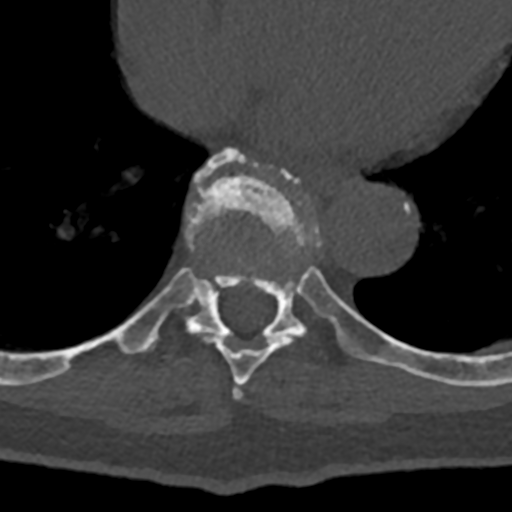
CT including the spine, one axial slice; position 681 of 797 along the scan axis; 120 kVp; bone window (W 1800 / L 400 HU); 0.5 mm slice thickness; 512 × 512 image matrix. Male patient, age 74 years. Case-level facts recorded for this patient, not image findings: primary cancer: renal; vertebrae with lytic lesions (as recorded): T10, L1, L2, L3, L4, L5.
Outlined on this slice (semi-automatically segmented with operator editing):
- T7 vertebra: bounding box <233,384,243,399> (left, top, right, bottom; pixels)
- T8 vertebra: <71,208,340,385>
- T9 vertebra: <82,149,432,379>